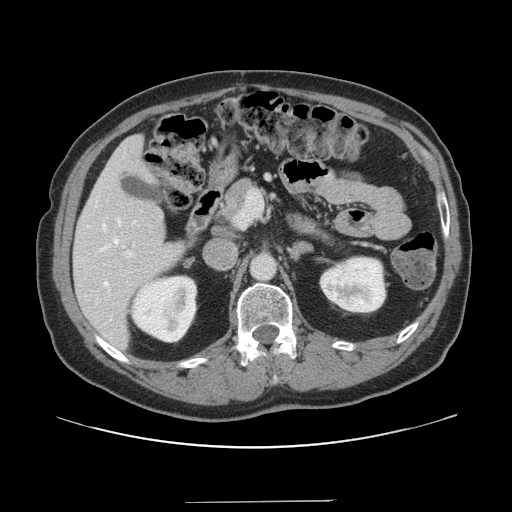
Contrast-enhanced abdominal CT, one axial slice. 120 kVp. Intravenous contrast given. Soft-tissue window (W 400 / L 40 HU). 2.5 mm slice thickness. 512 × 512 image matrix, field of view 399 × 399 mm. Male patient, age 63 years. Case-level facts recorded for this patient, not image findings: diagnosis: colorectal cancer liver metastases, imaged before liver resection; multiple liver metastases: no; largest metastasis: 2.1 cm.
Annotated regions visible in this slice (expert manual segmentation):
- hepatic veins: bounding box <102,218,121,287> (left, top, right, bottom; pixels)
- liver: <74,136,189,350>
- planned liver remnant (the part of the liver to remain after resection): <74,136,187,350>
- portal vein (with intrahepatic branches): <123,192,263,258>